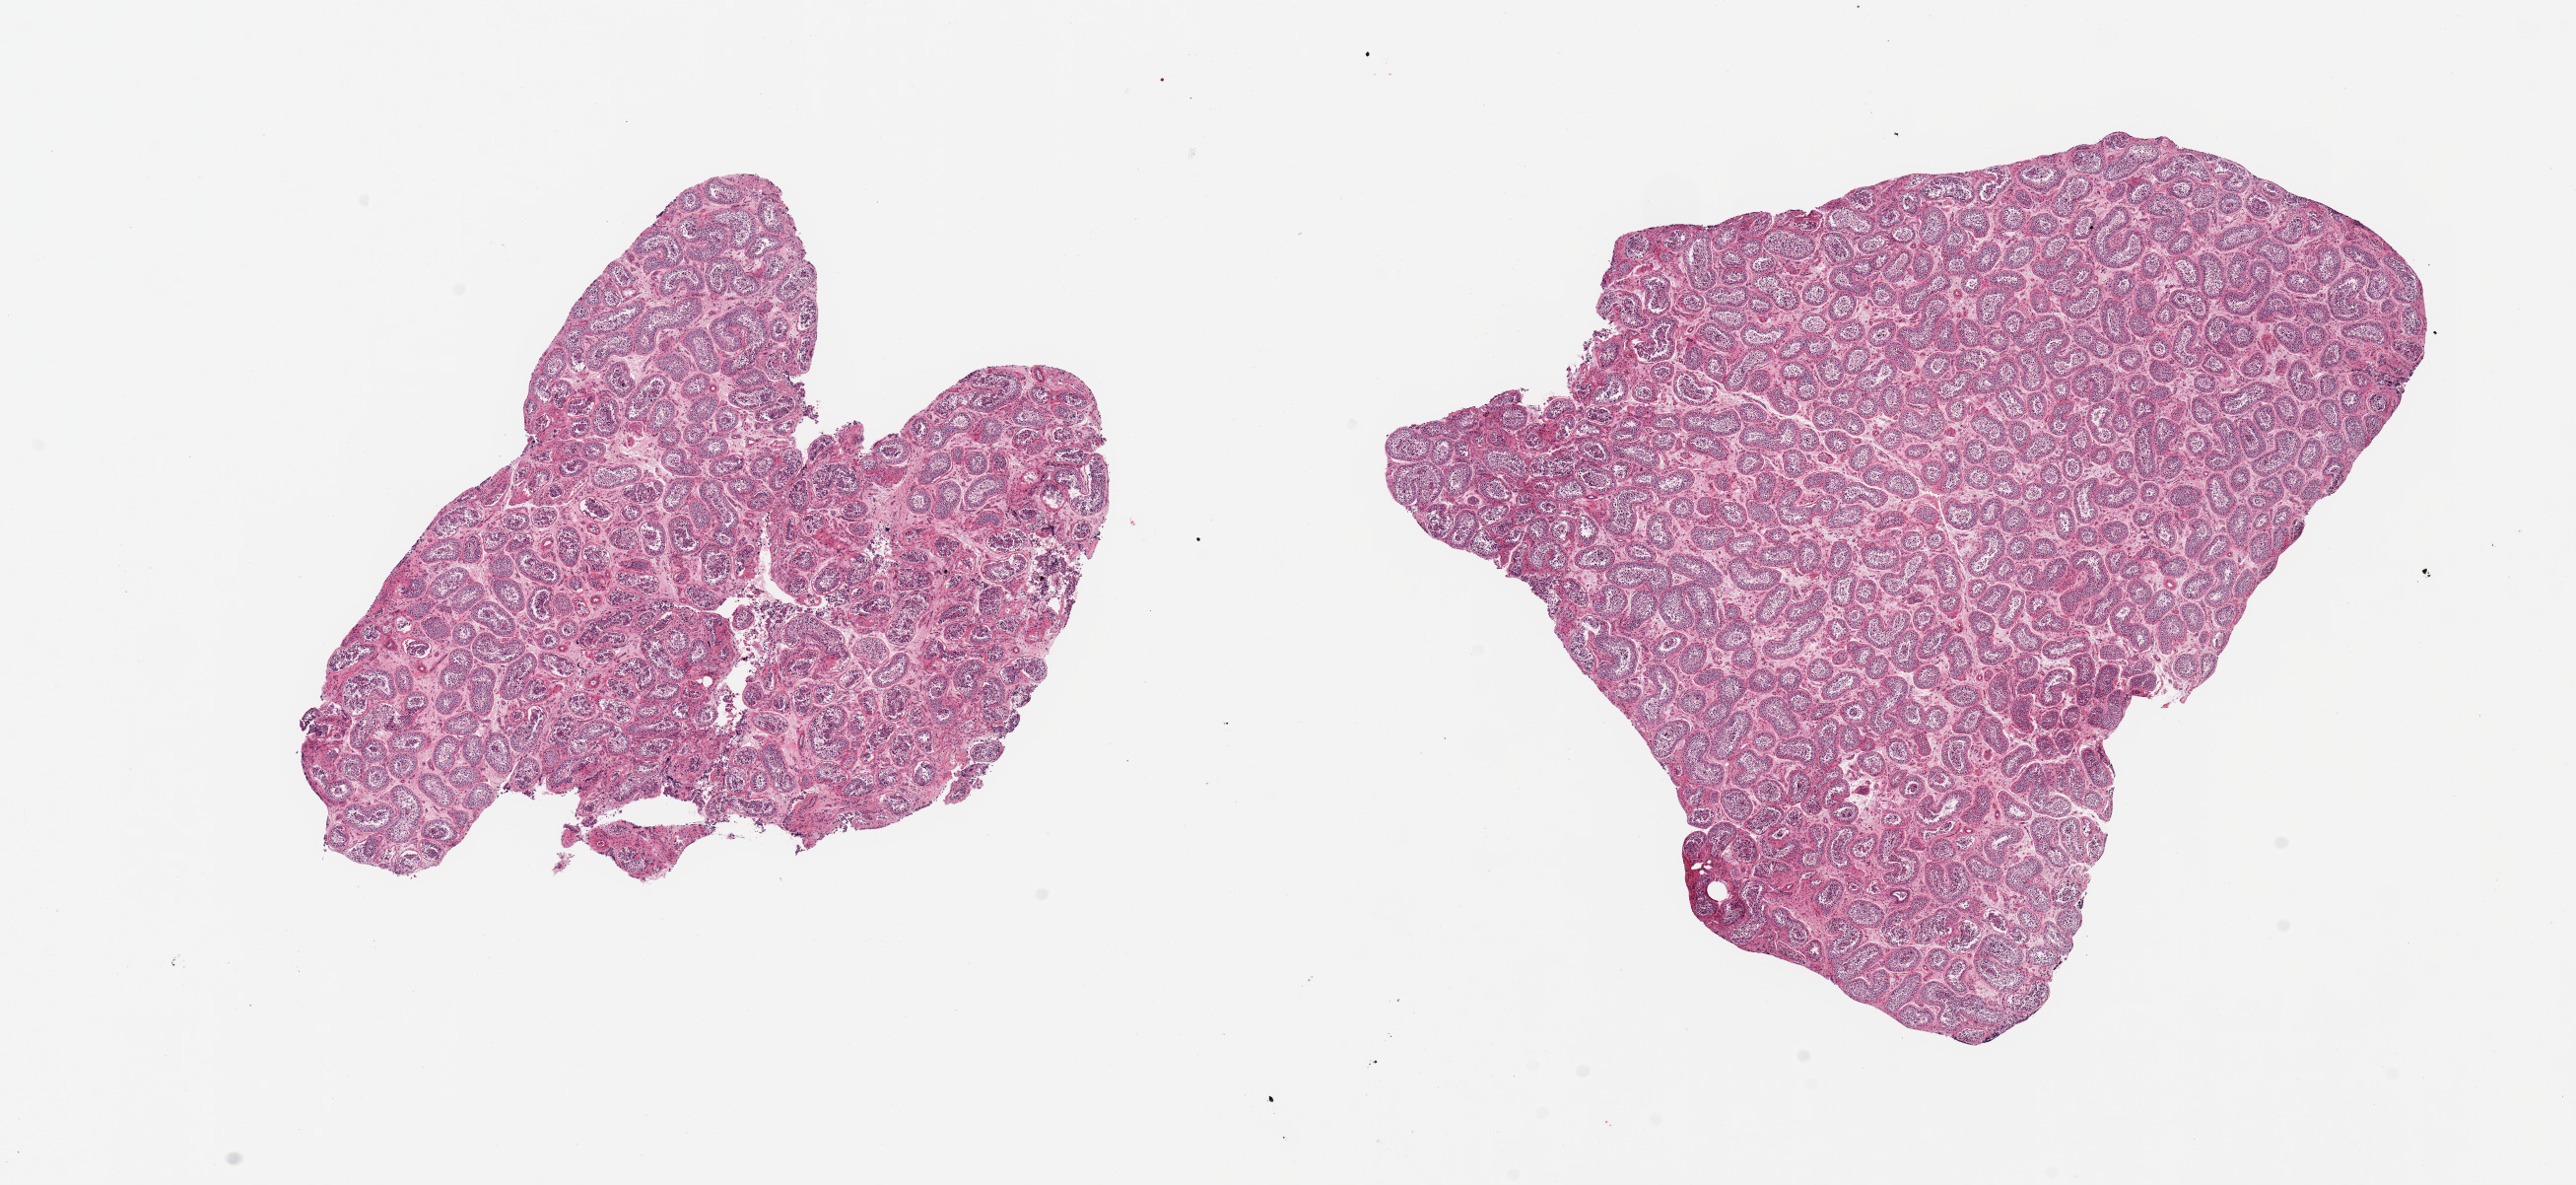
H&E whole-slide image, whole scanned area (about 20.7 x 9.5 mm) shown as a low-resolution overview. PAXgene-fixed, paraffin-embedded tissue. Section of testis (target tissue). Donor tissue sample. Male donor.
Reviewer comment on this tissue sample: 2 pieces, spermatogenesis is present.